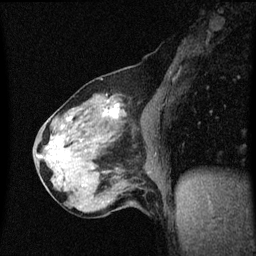
Breast MRI (dynamic contrast-enhanced), one sagittal slice. Position 24 of 60 along the scan axis. Dynamic contrast-enhanced series, image 2 of 3 at this slice position (ordered by acquisition). 1.5 T. TE 4.2 ms, TR 8.4 ms. 2 mm slice thickness. 256 × 256 image matrix, field of view 200 × 200 mm. Patient: female, 64 years. Case-level facts recorded for this patient, not image findings: setting: breast cancer imaged before/during neoadjuvant chemotherapy; receptor status: HR-positive, HER2-negative.
Outlined on this slice (semi-automatic segmentation, software-assisted and operator-edited):
- analysis volume of interest (the breast-tissue region the enhancement analysis was run in; not a lesion): bounding box [x1, y1, x2, y2] px = [56, 96, 127, 175]
- tumour enhancement mask (voxels above the 70 % enhancement threshold inside the analysis volume of interest): [105, 104, 120, 117]